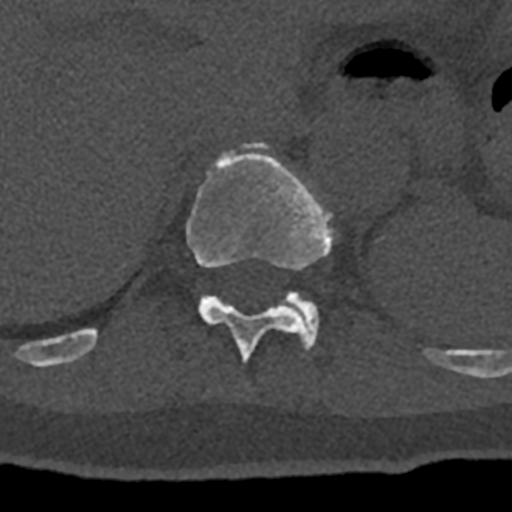
CT including the spine, one axial slice. Slice 538 of 797 in the series (ordered by position). Reconstruction kernel Br40s/3. Bone window (W 1800 / L 400 HU). 512 × 512 image matrix, field of view 160 × 160 mm. Patient: male, 74 years. From the clinical record (not read from this slice): primary cancer: renal.
Outlined on this slice (semi-automatic segmentation, software-assisted and operator-edited):
- T11 vertebra: box from (x=70, y=142) to (x=432, y=365) px
- T12 vertebra: (x=281, y=291)–(x=319, y=348)